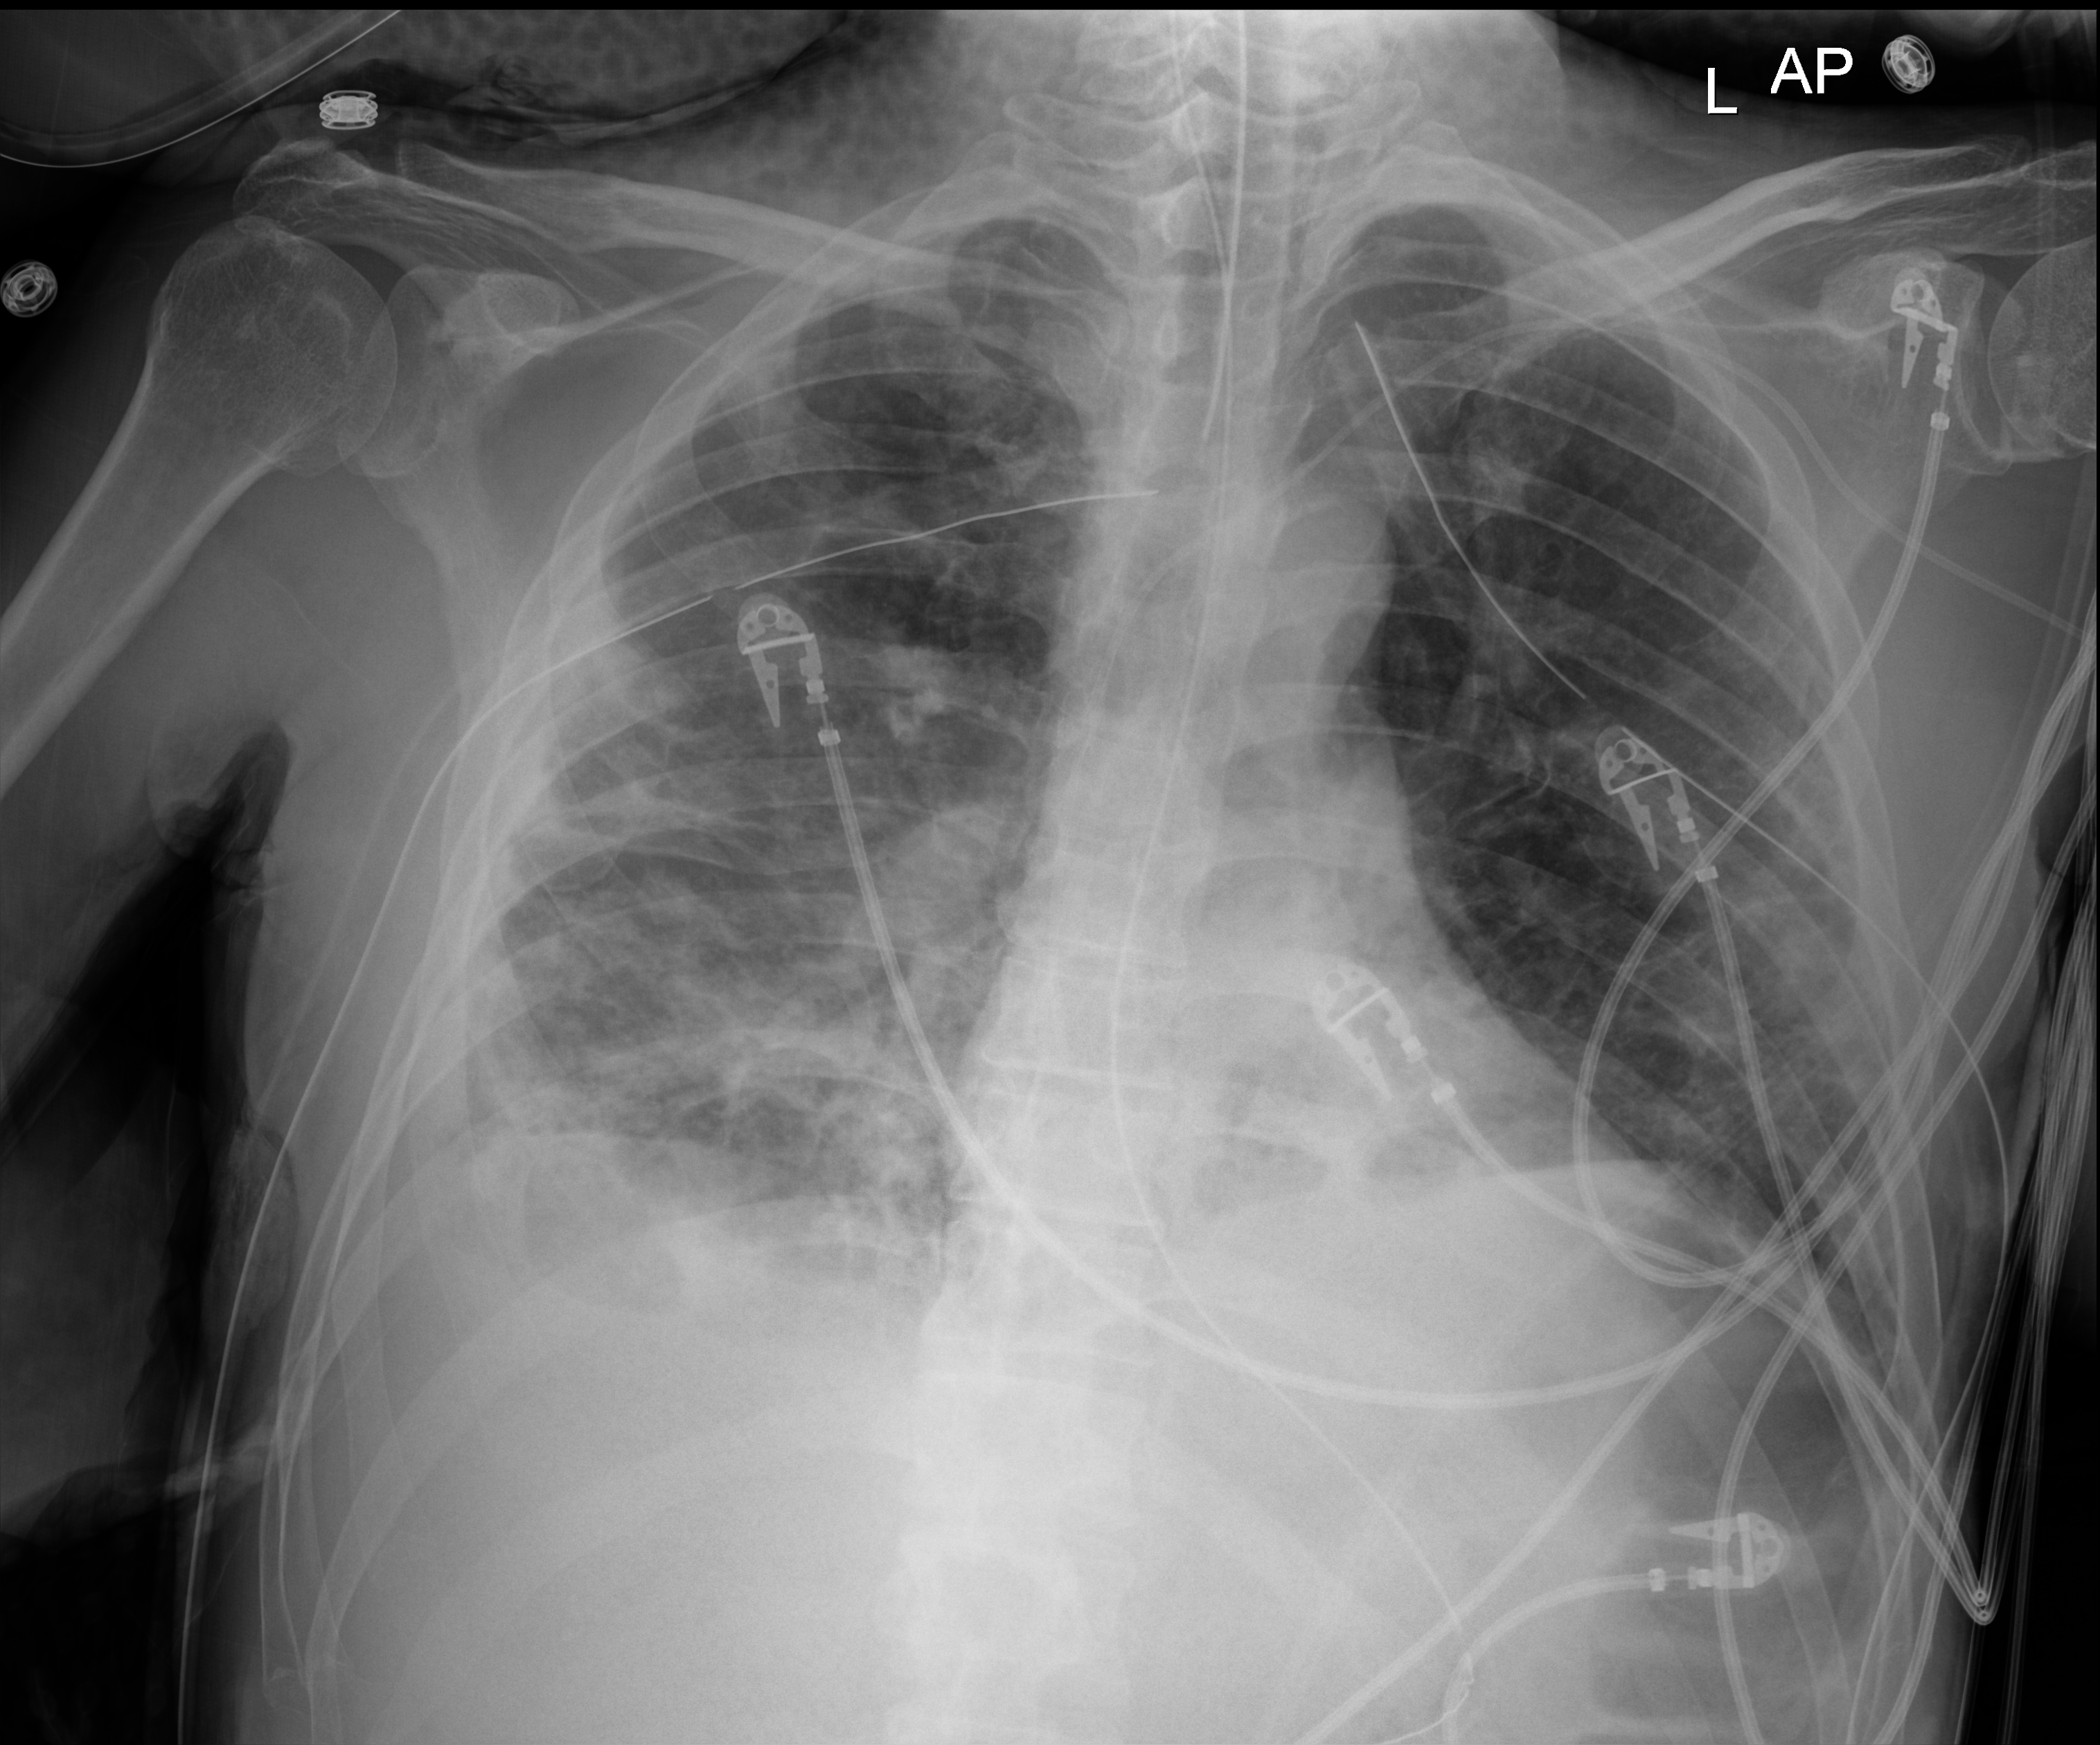
Portable chest radiograph. Male patient hospitalised with COVID-19, age 18–59 years.
Admission-level facts for this patient (not findings on this image; timing relative to this image not recorded):
- length of hospital stay: 96 days
- chronic kidney disease (admission record): no
- admitted to intensive care during this hospital stay: yes